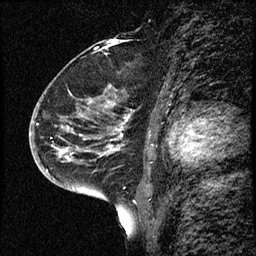
Breast MRI (dynamic contrast-enhanced), one sagittal slice; slice 40 of 68 in the series (ordered by position); dynamic contrast-enhanced study with each time point stored as its own series, time point 2 of 3 at this slice position (early post-contrast, ordered by acquisition time); 1.5 T; TE 4.2 ms, TR 17.6 ms; 2 mm slice thickness; 256 × 256 image matrix, field of view 200 × 200 mm. Patient: female, 52 years. Case-level facts recorded for this patient, not image findings: setting: breast cancer imaged before/during neoadjuvant chemotherapy; receptor status: HER2-positive.
Annotated regions visible in this slice (semi-automatically segmented with operator editing):
- analysis volume of interest (the breast-tissue region the enhancement analysis was run in; not a lesion): box from (x=50, y=61) to (x=132, y=184) px
- tumour enhancement mask (voxels above the 100 % enhancement threshold inside the analysis volume of interest): (x=60, y=101)–(x=122, y=160)